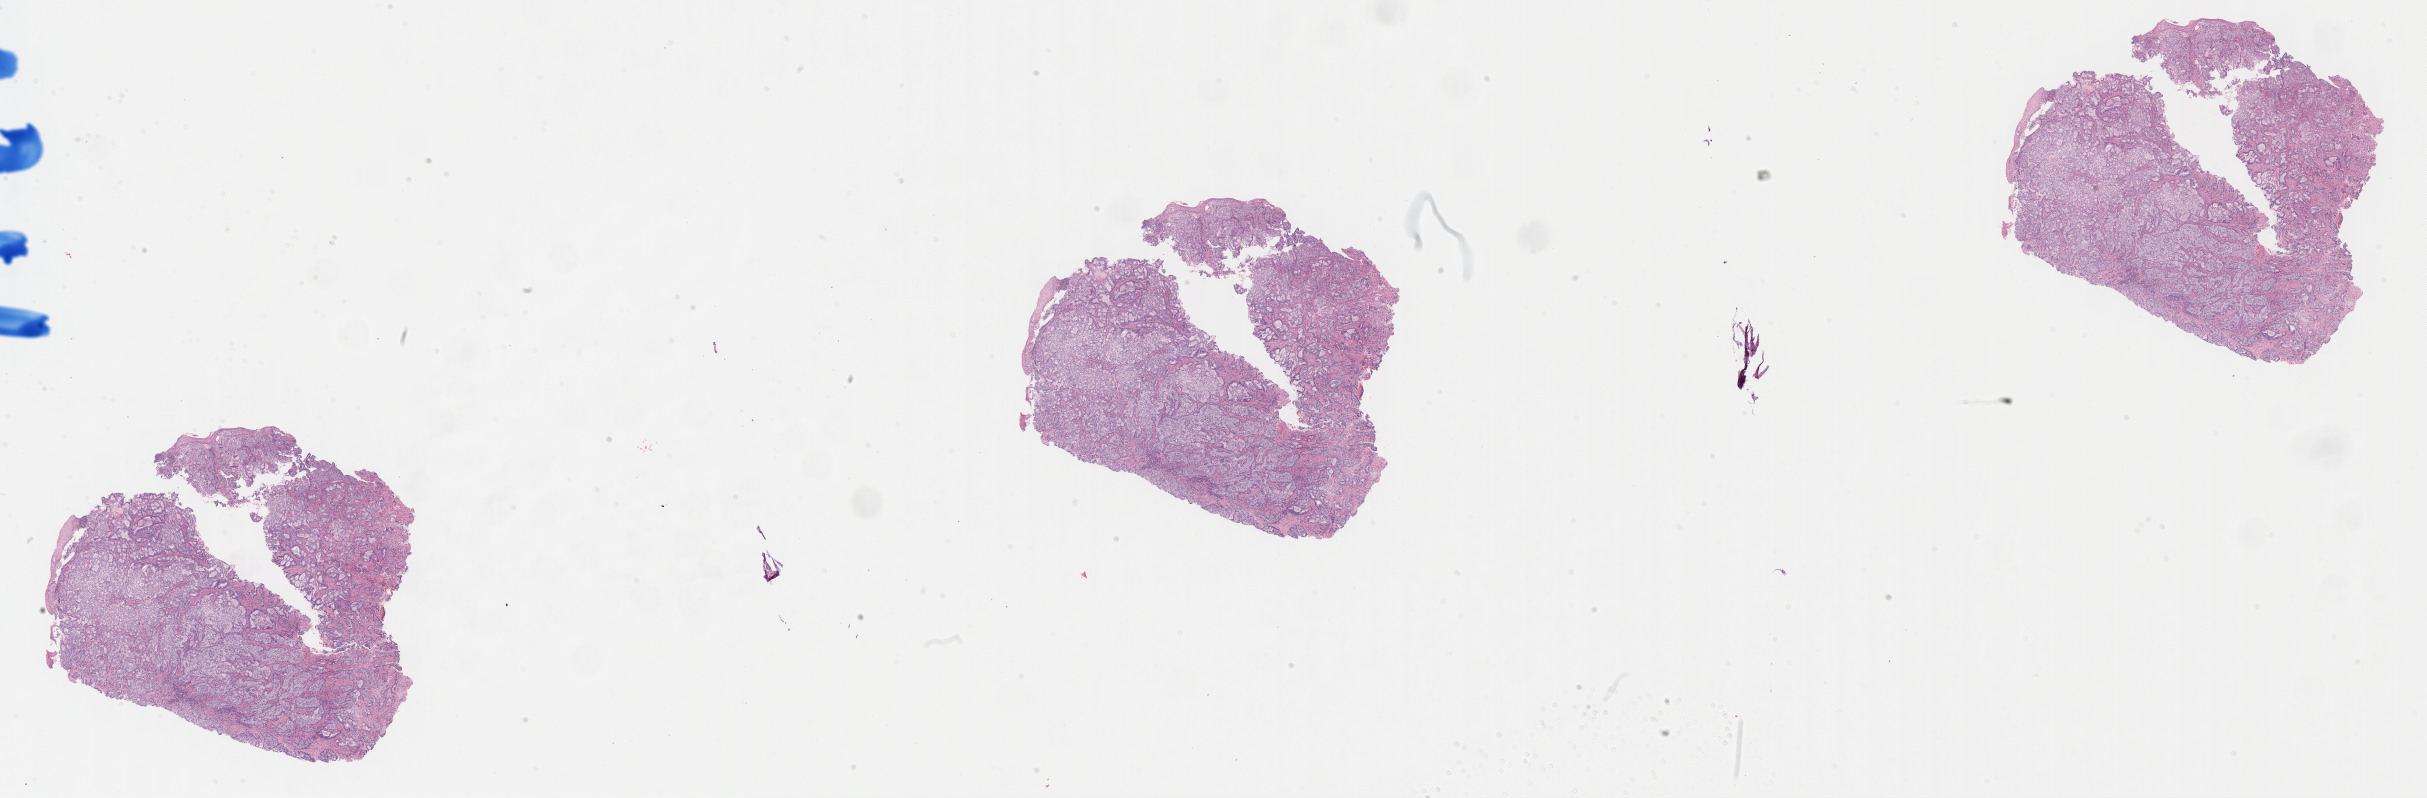
Whole-slide image, haematoxylin and eosin stain, shown as a low-resolution overview of the whole scanned area (about 39.3 x 12.9 mm); tumor tissue; site: cervix. Female patient, aged 28.
Diagnosis: Adenocarcinoma, NOS.